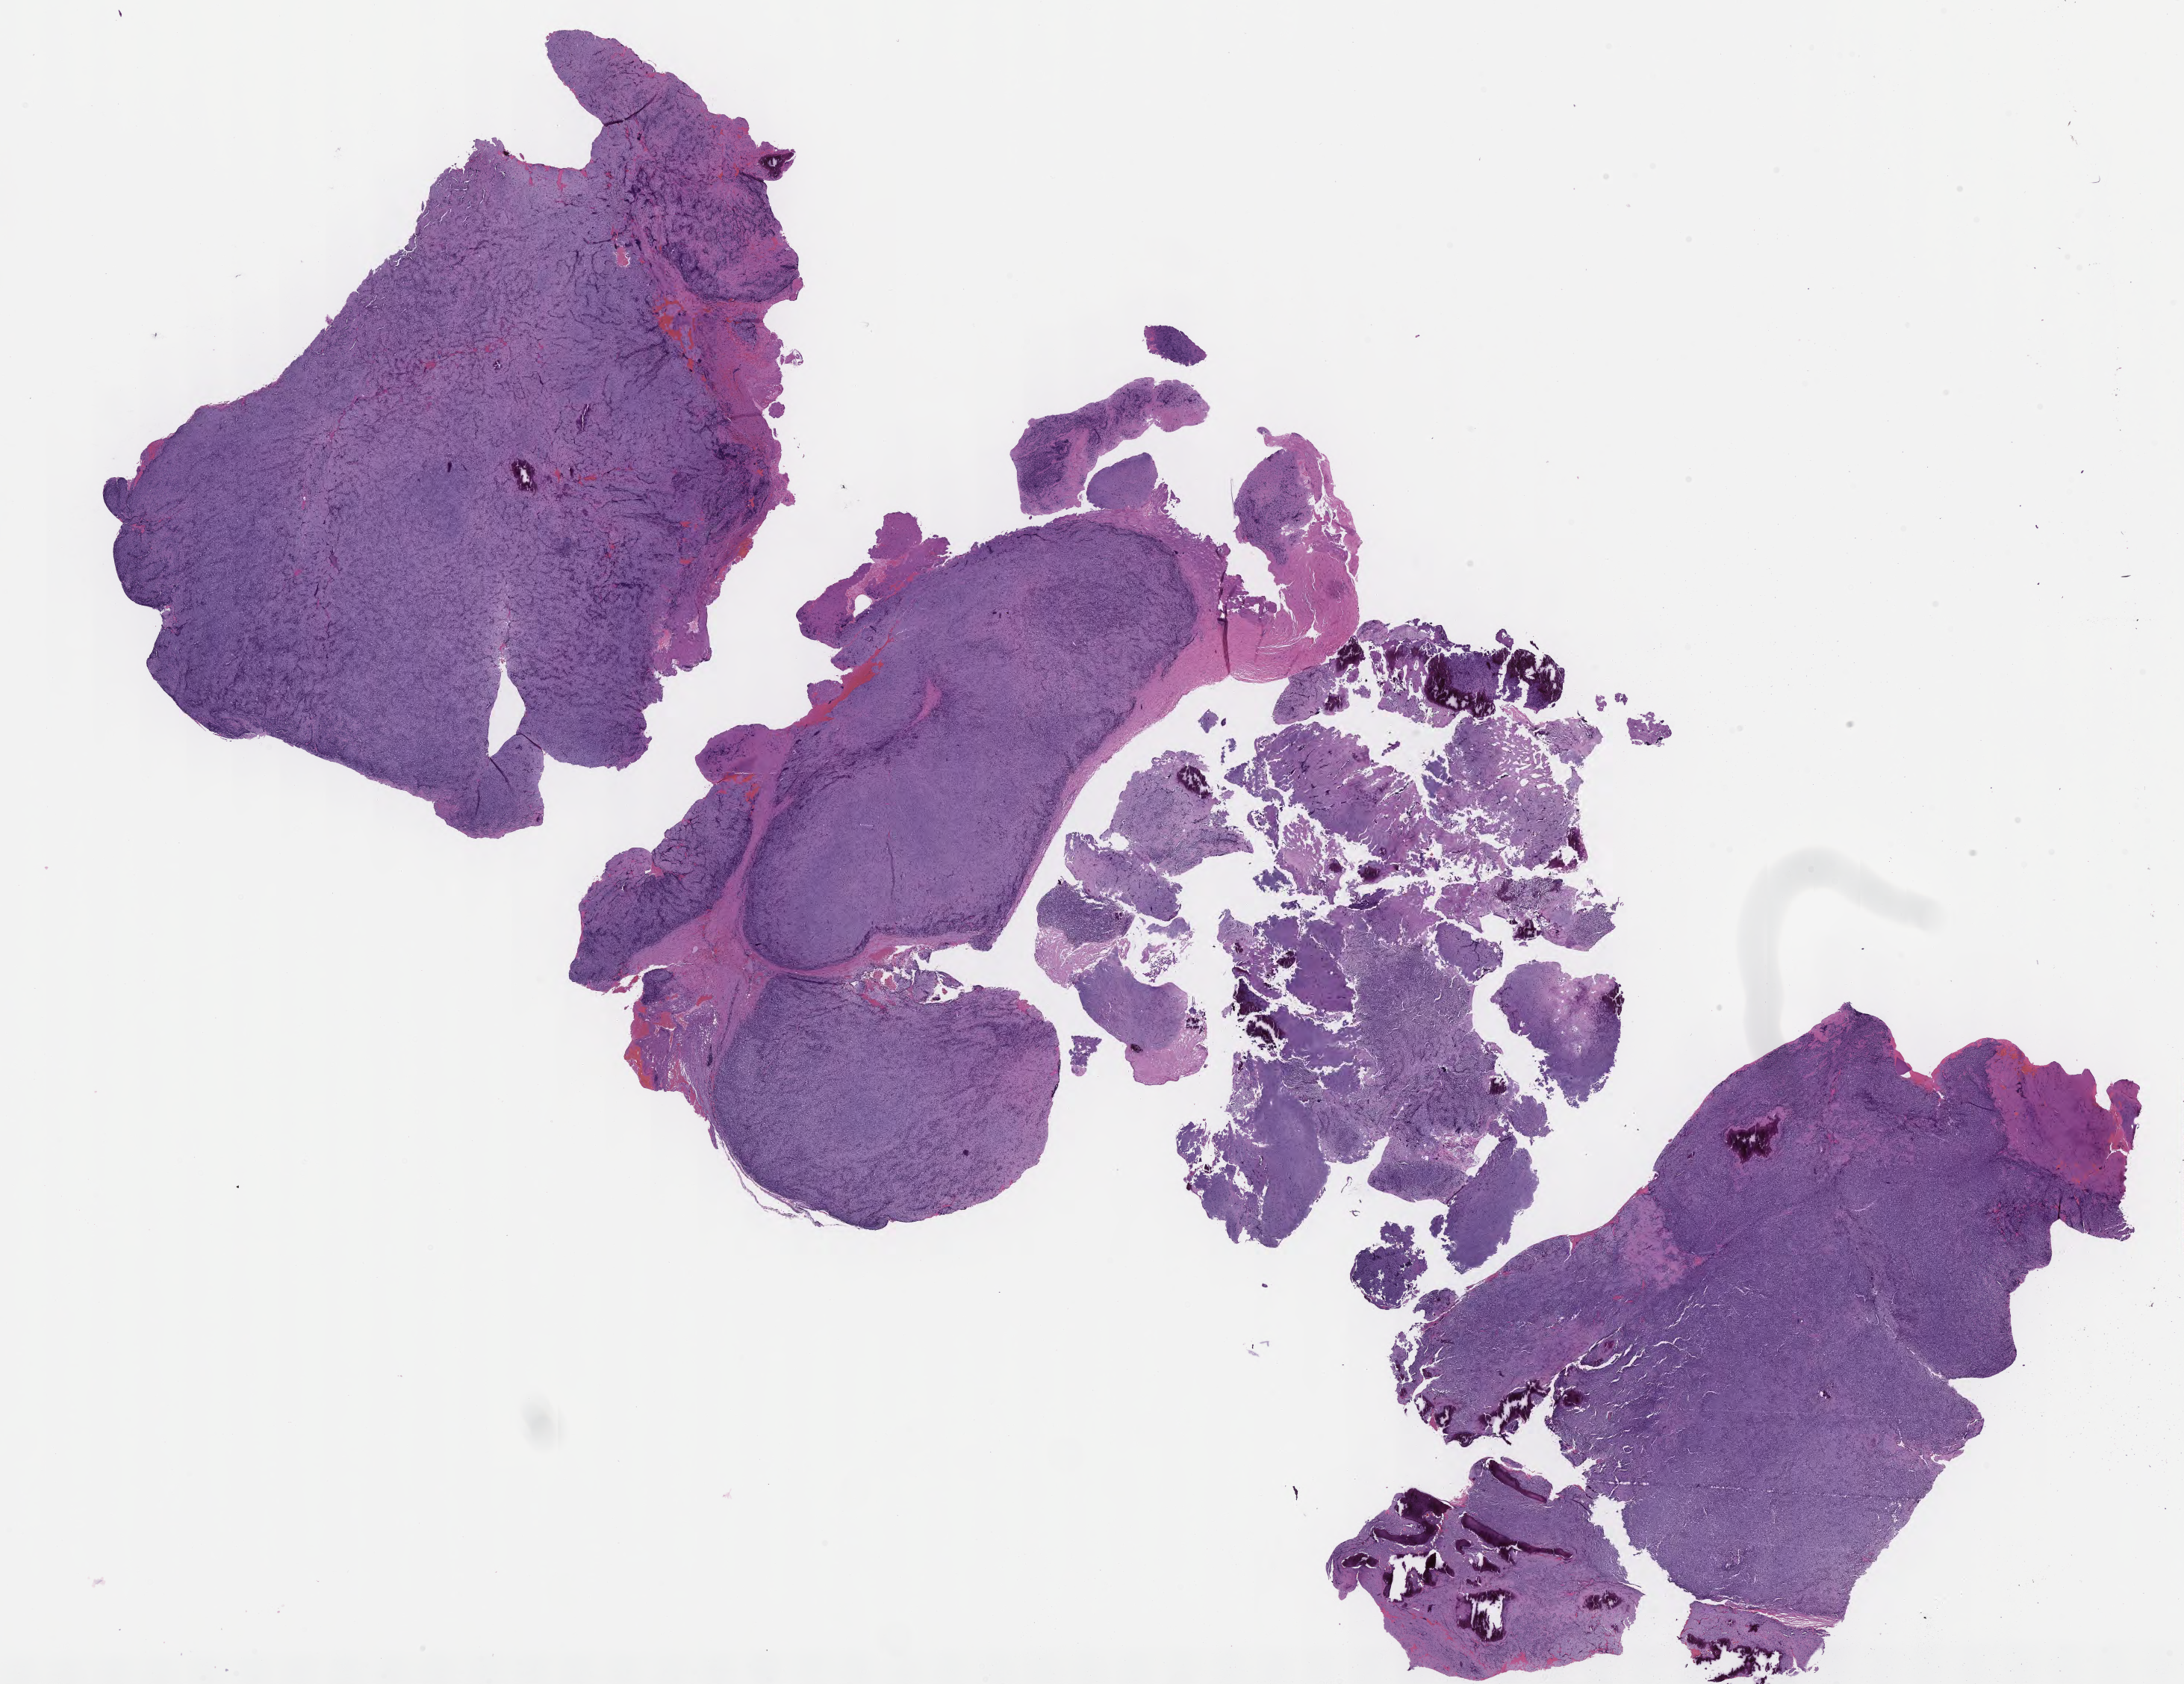
Digitized haematoxylin and eosin-stained section of tumor tissue from the thorax, a low-resolution overview of the entire scanned area, about 23.6 x 18.2 mm. FFPE section. Patient female; age 156 months (13 years).
Diagnosis (ICD-O-3 morphology term): Mesenchymal chondrosarcoma.